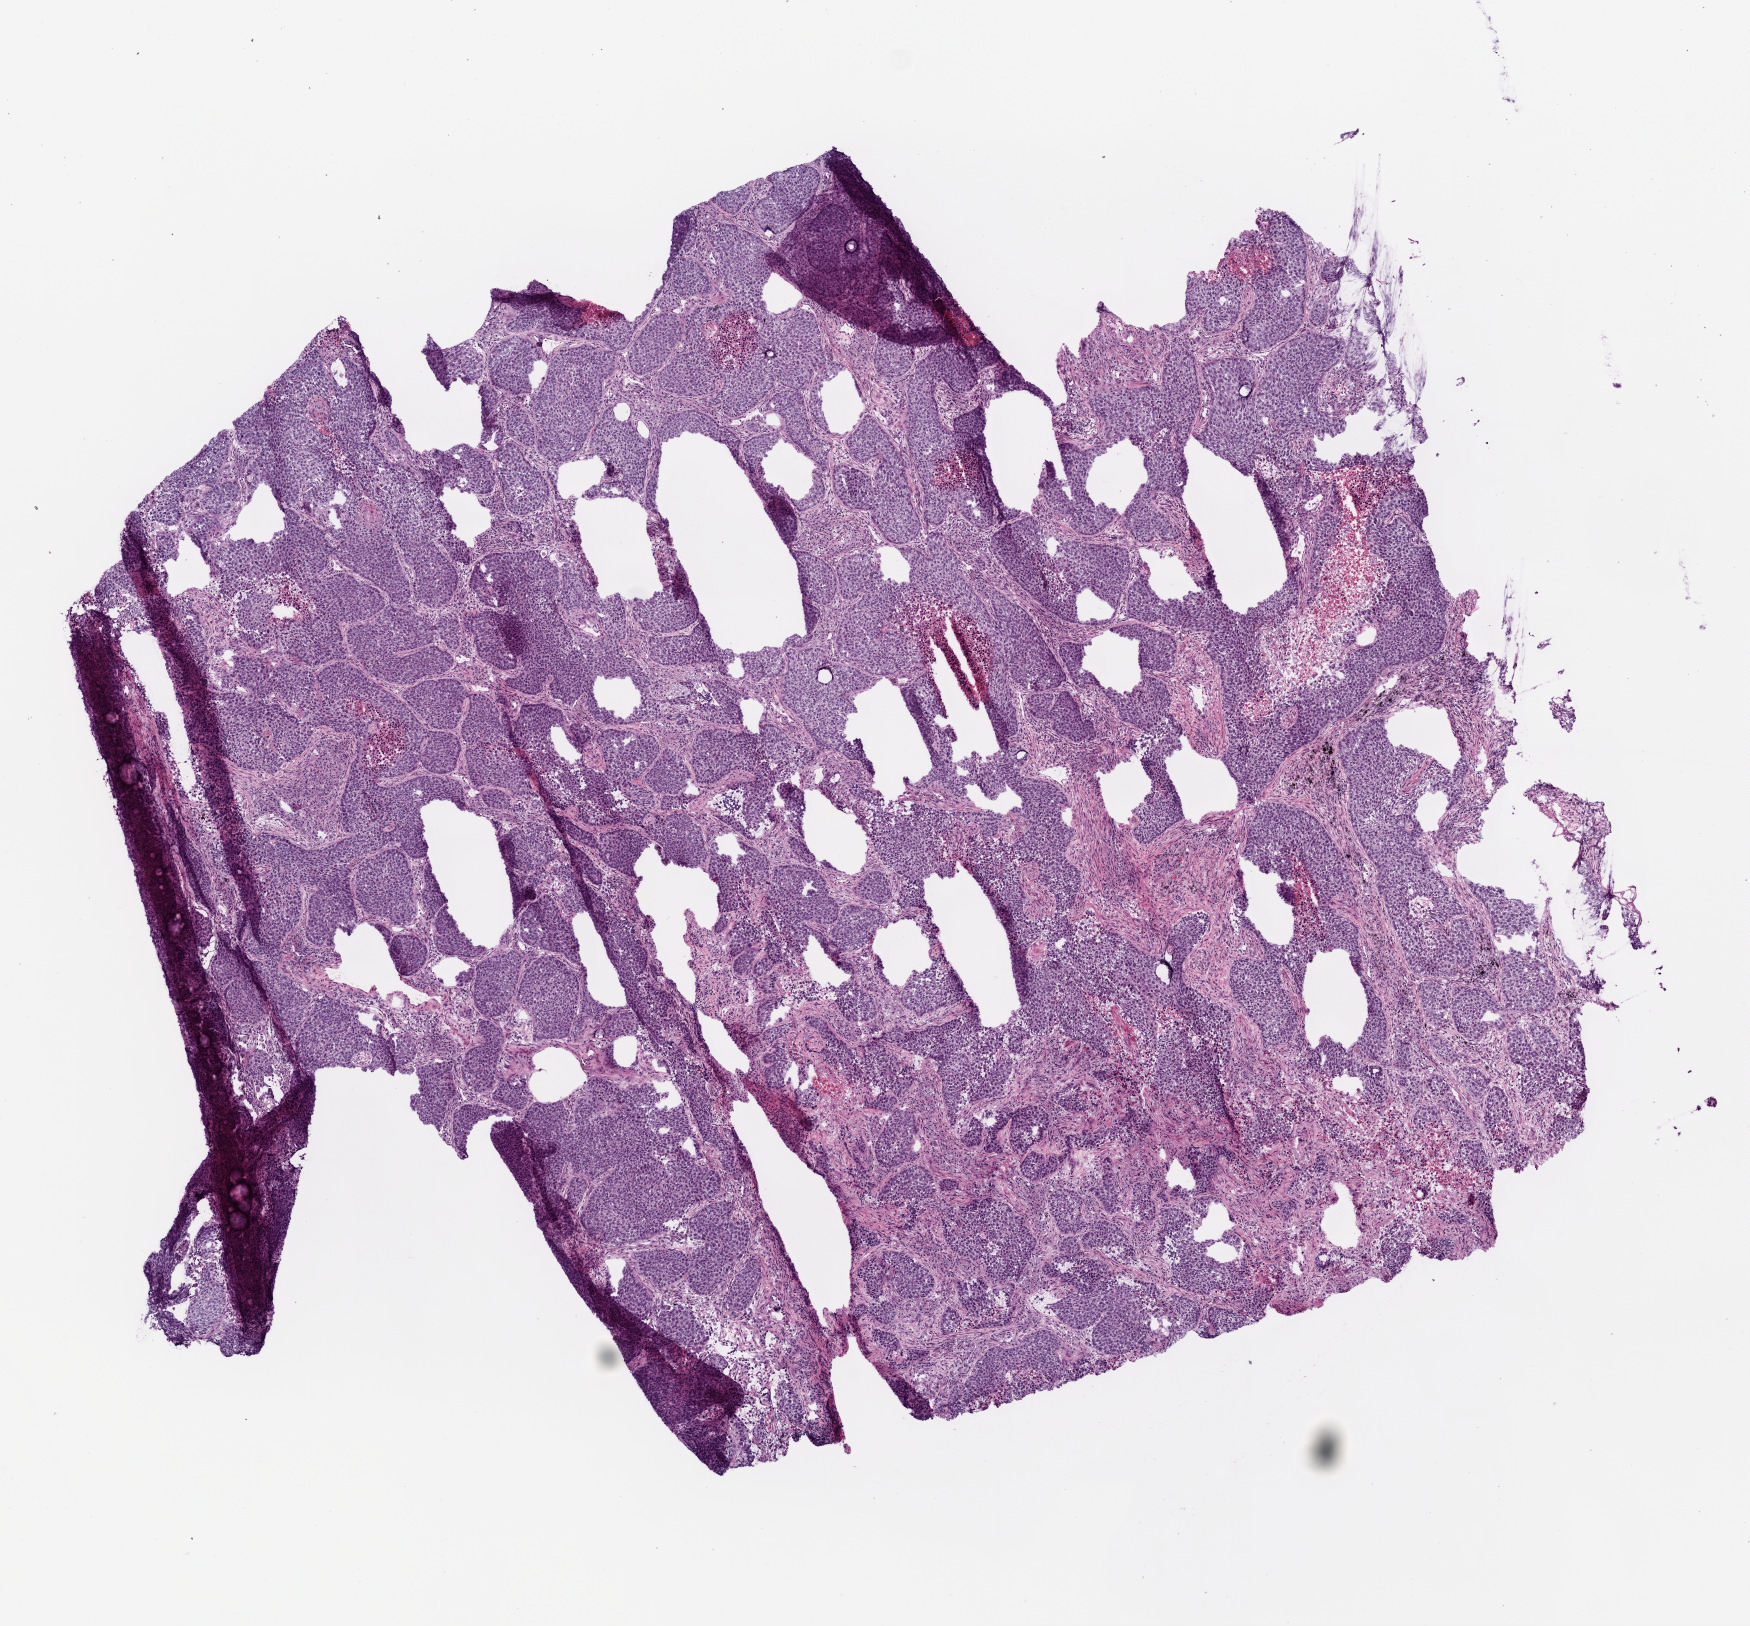
H&E-stained whole-slide image — low-resolution overview of the scanned area, about 7.0 x 6.5 mm (from a 20x scan), frozen section, lung, primary tumour sample. Male, age 58 years at initial diagnosis. Composition of this section per pathologist review: tumour cells 82%, tumour nuclei 75%, normal cells 0%, stromal cells 10%, necrosis 8%.
Laterality: left. TNM: T3 N1 M0. Pathologic diagnosis: Squamous cell carcinoma, NOS (upper lobe, lung). AJCC pathologic stage: IIIA.